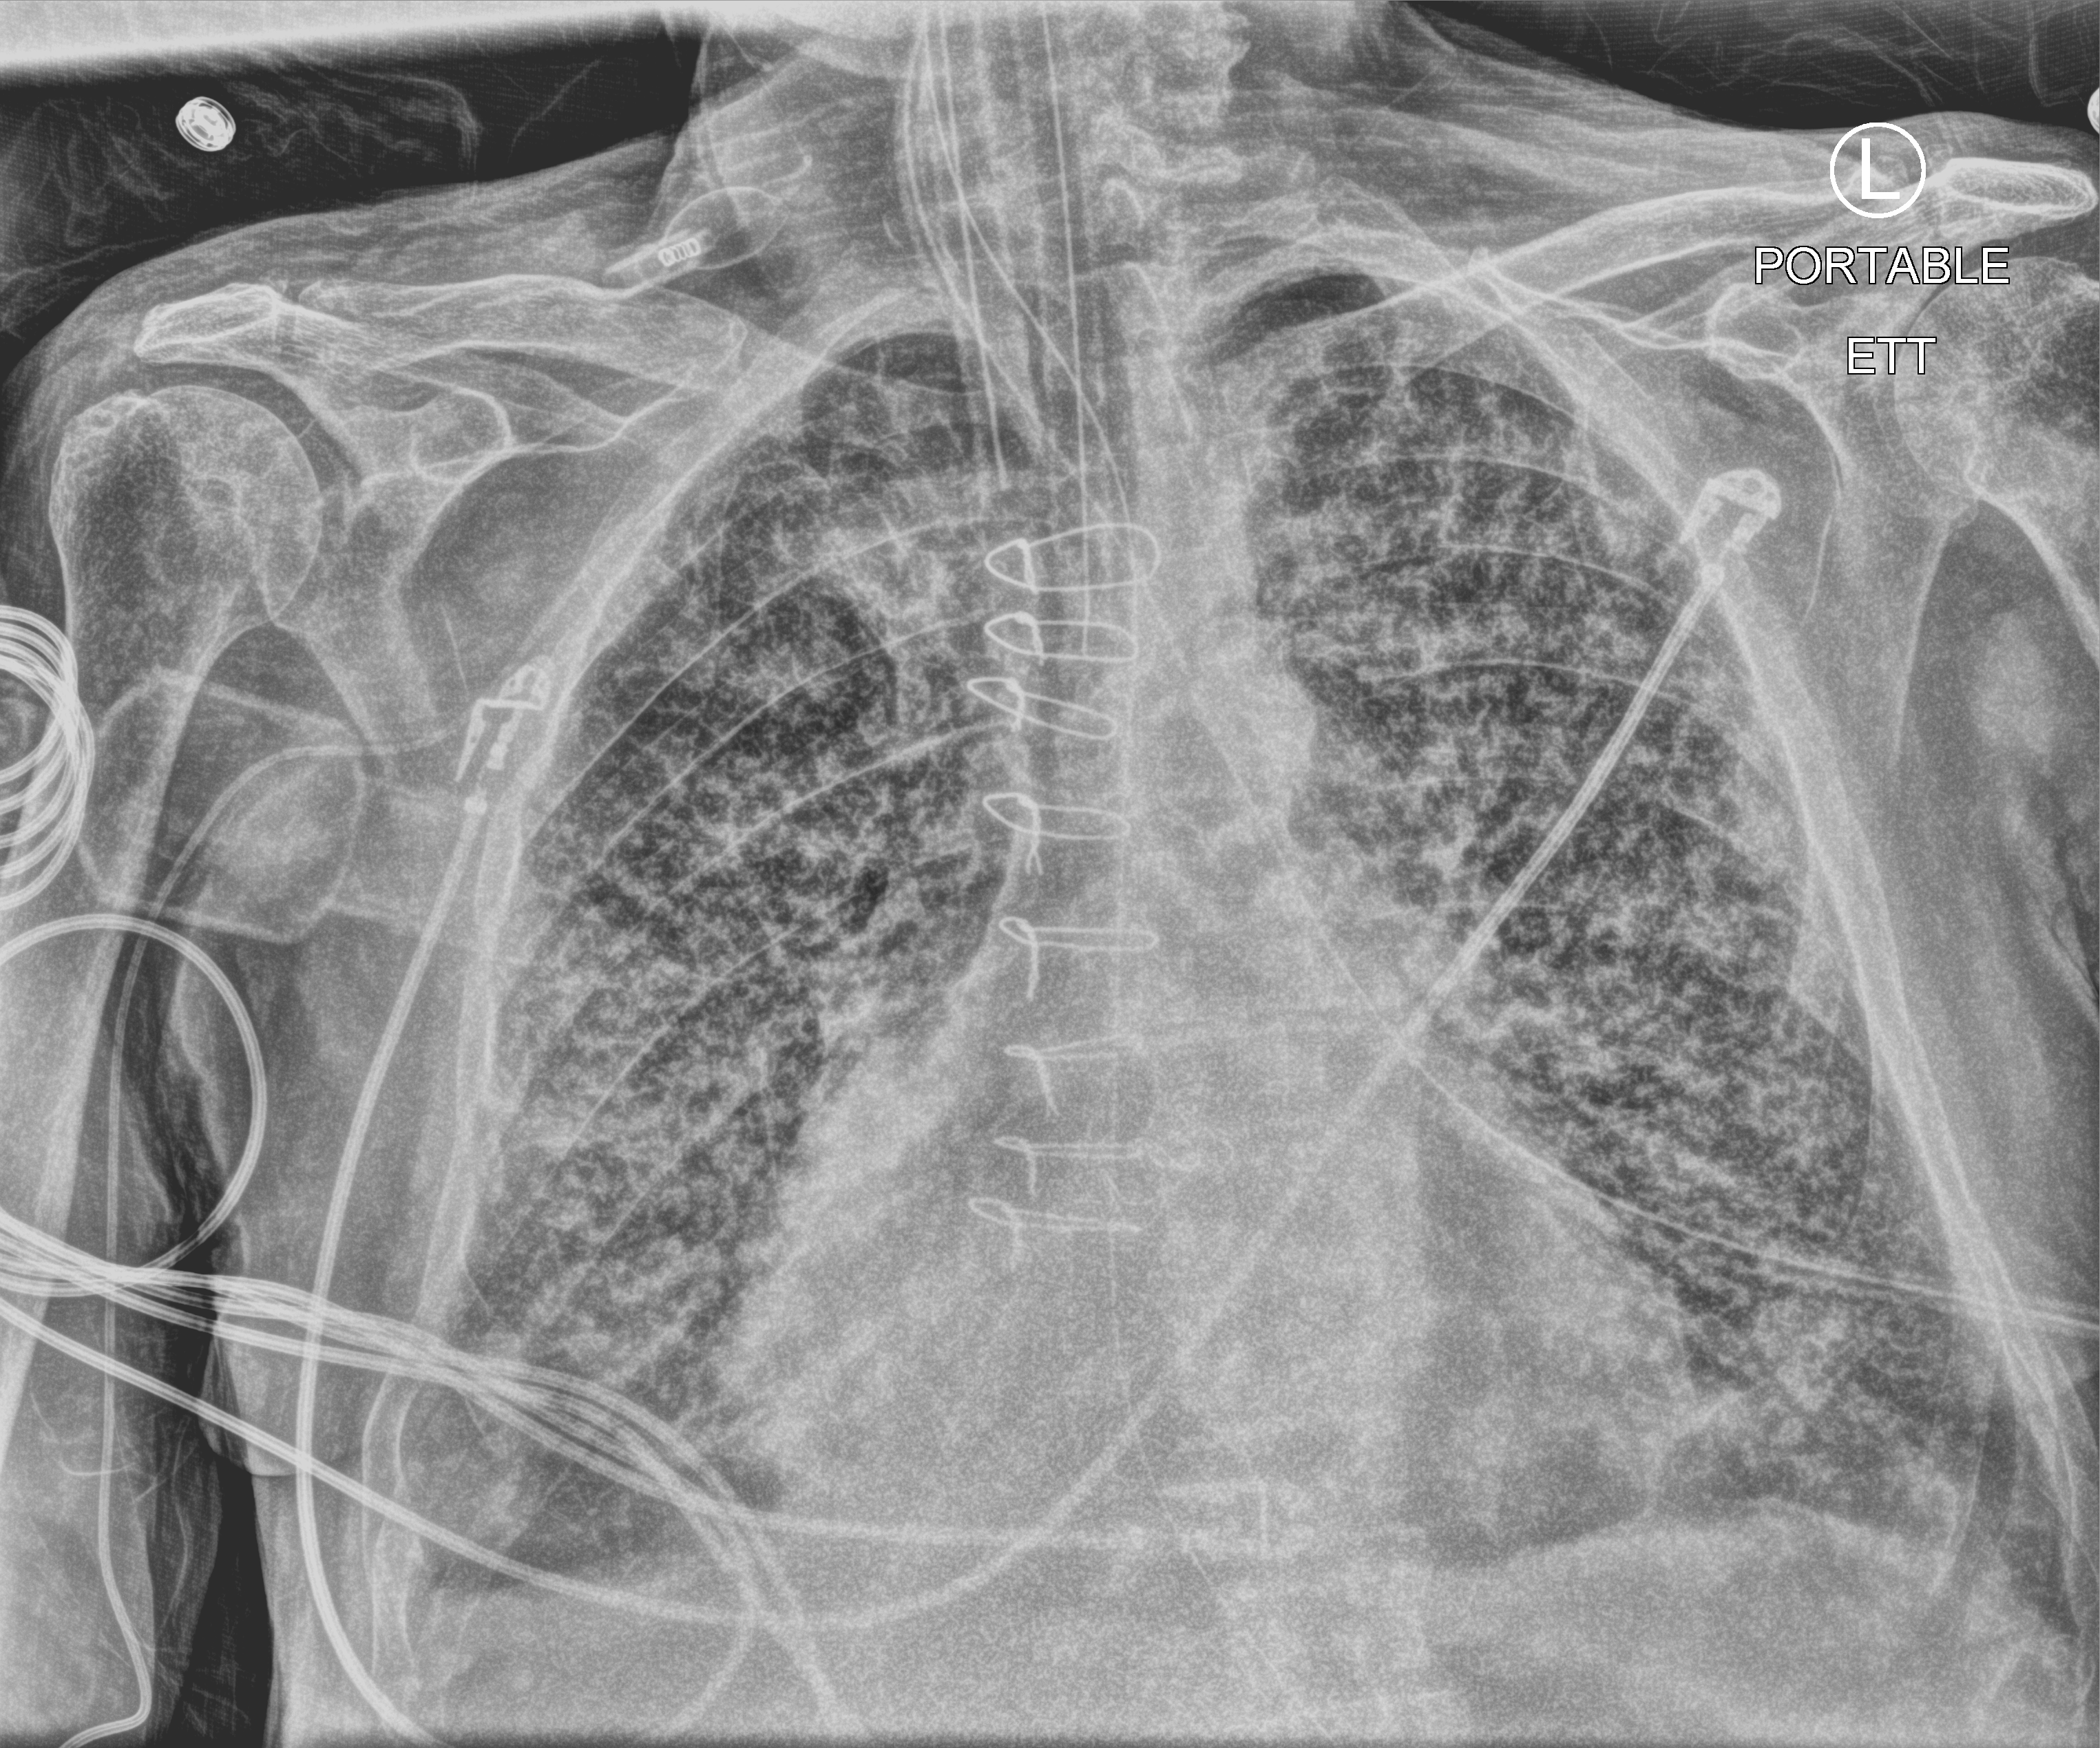
Portable chest radiograph, anteroposterior (AP) projection. Patient hospitalised with COVID-19; male, aged 75–90 years.
Admission-level facts for this patient (not findings on this image; timing relative to this image not recorded):
- mechanically ventilated during this hospital stay: yes